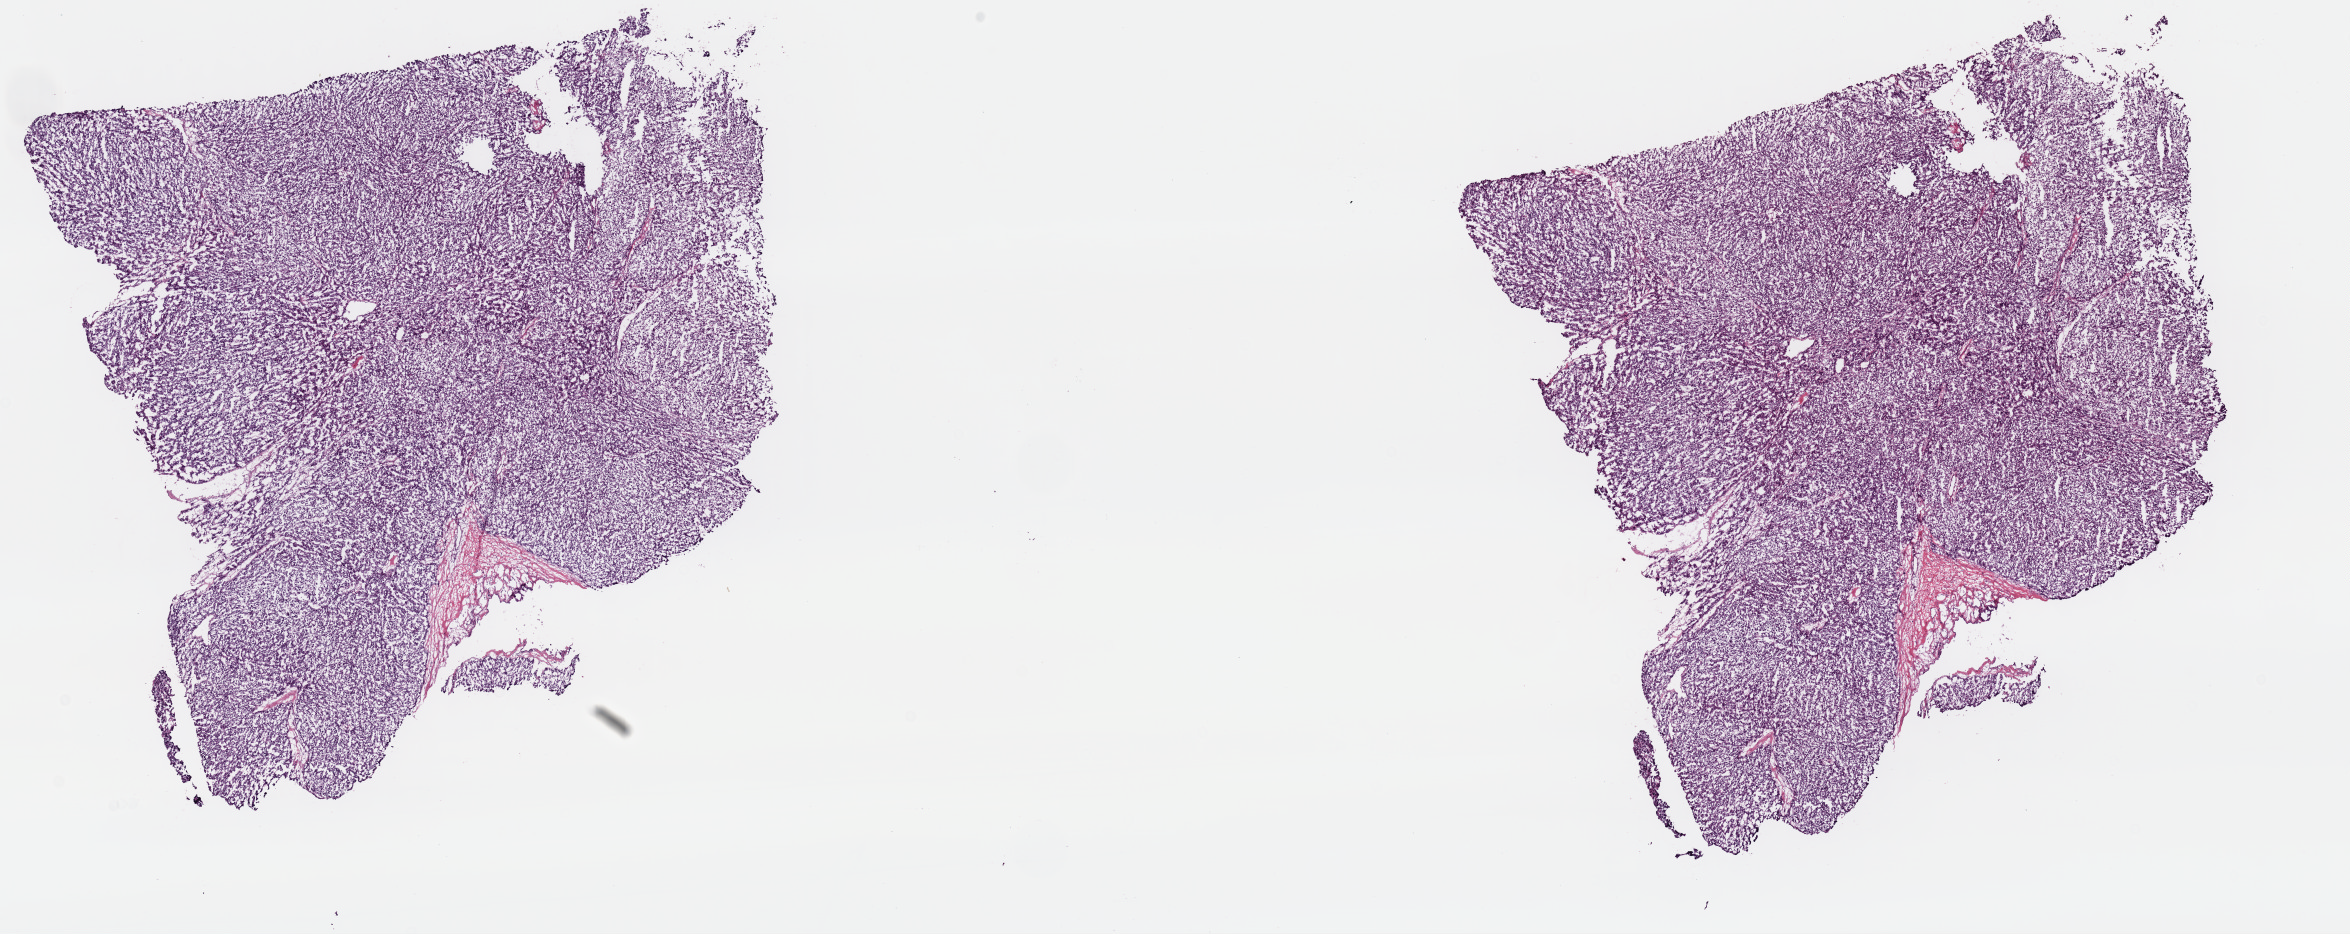
Digitized Hematoxylin and eosin (H&E) stained tissue section (whole slide), a low-resolution overview of the entire scanned area, about 18.6 x 7.4 mm, frozen section from the top of the tissue portion, liver, primary tumour sample. Male, age 69 years at initial diagnosis. Composition of this section per pathologist review: tumour cells 90%, tumour nuclei 95%.
Pathologic diagnosis: Hepatocellular carcinoma, NOS.